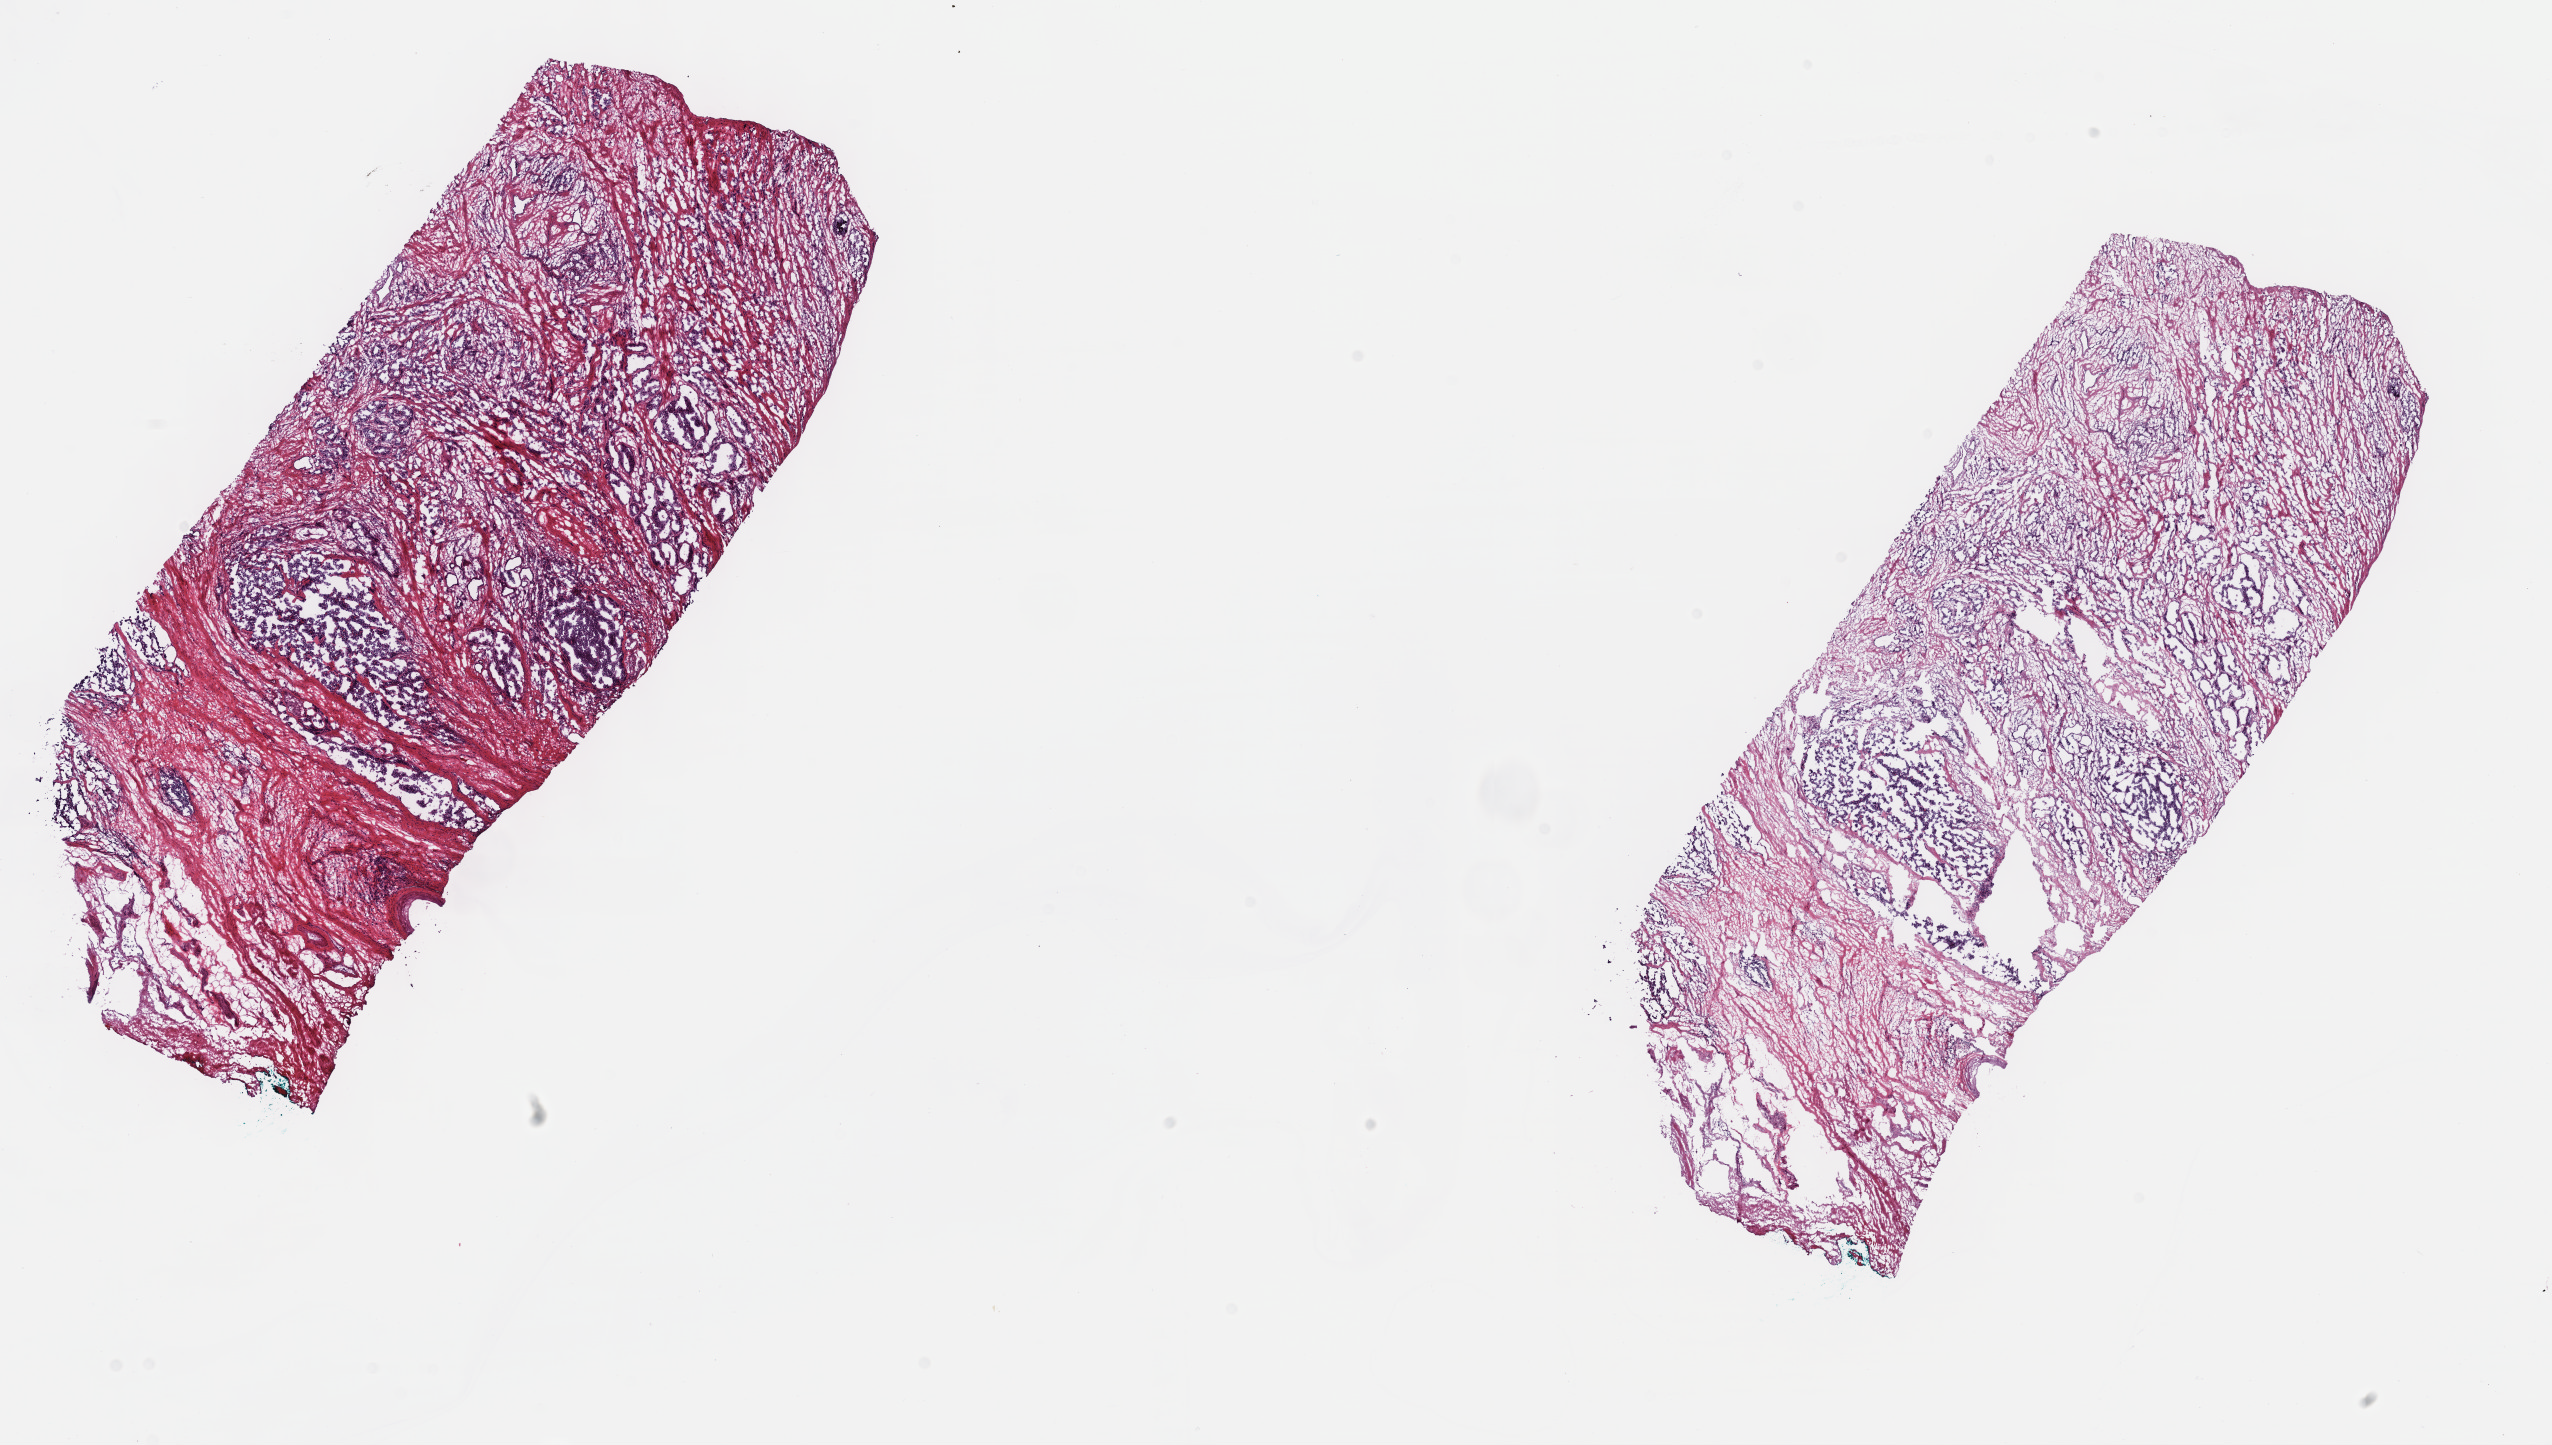
Digitized H&E tissue section (whole slide), low-resolution overview of the scanned area, about 20.6 x 11.7 mm (slide scanned at 40x). Frozen section from the top of the tissue portion. Sample: primary tumour, prostate. Male, age 65 years at initial diagnosis. Gleason score: 9 (5+4). Composition of this section per pathologist review: tumour cells 60%, tumour nuclei 70%, normal cells 0%, stromal cells 40%, necrosis 0%. Inflammatory infiltration, as recorded: lymphocyte infiltration 0%, monocyte infiltration 0%, neutrophil infiltration 0%.
- laterality: bilateral
- pathologic diagnosis: Adenocarcinoma, NOS (prostate gland)